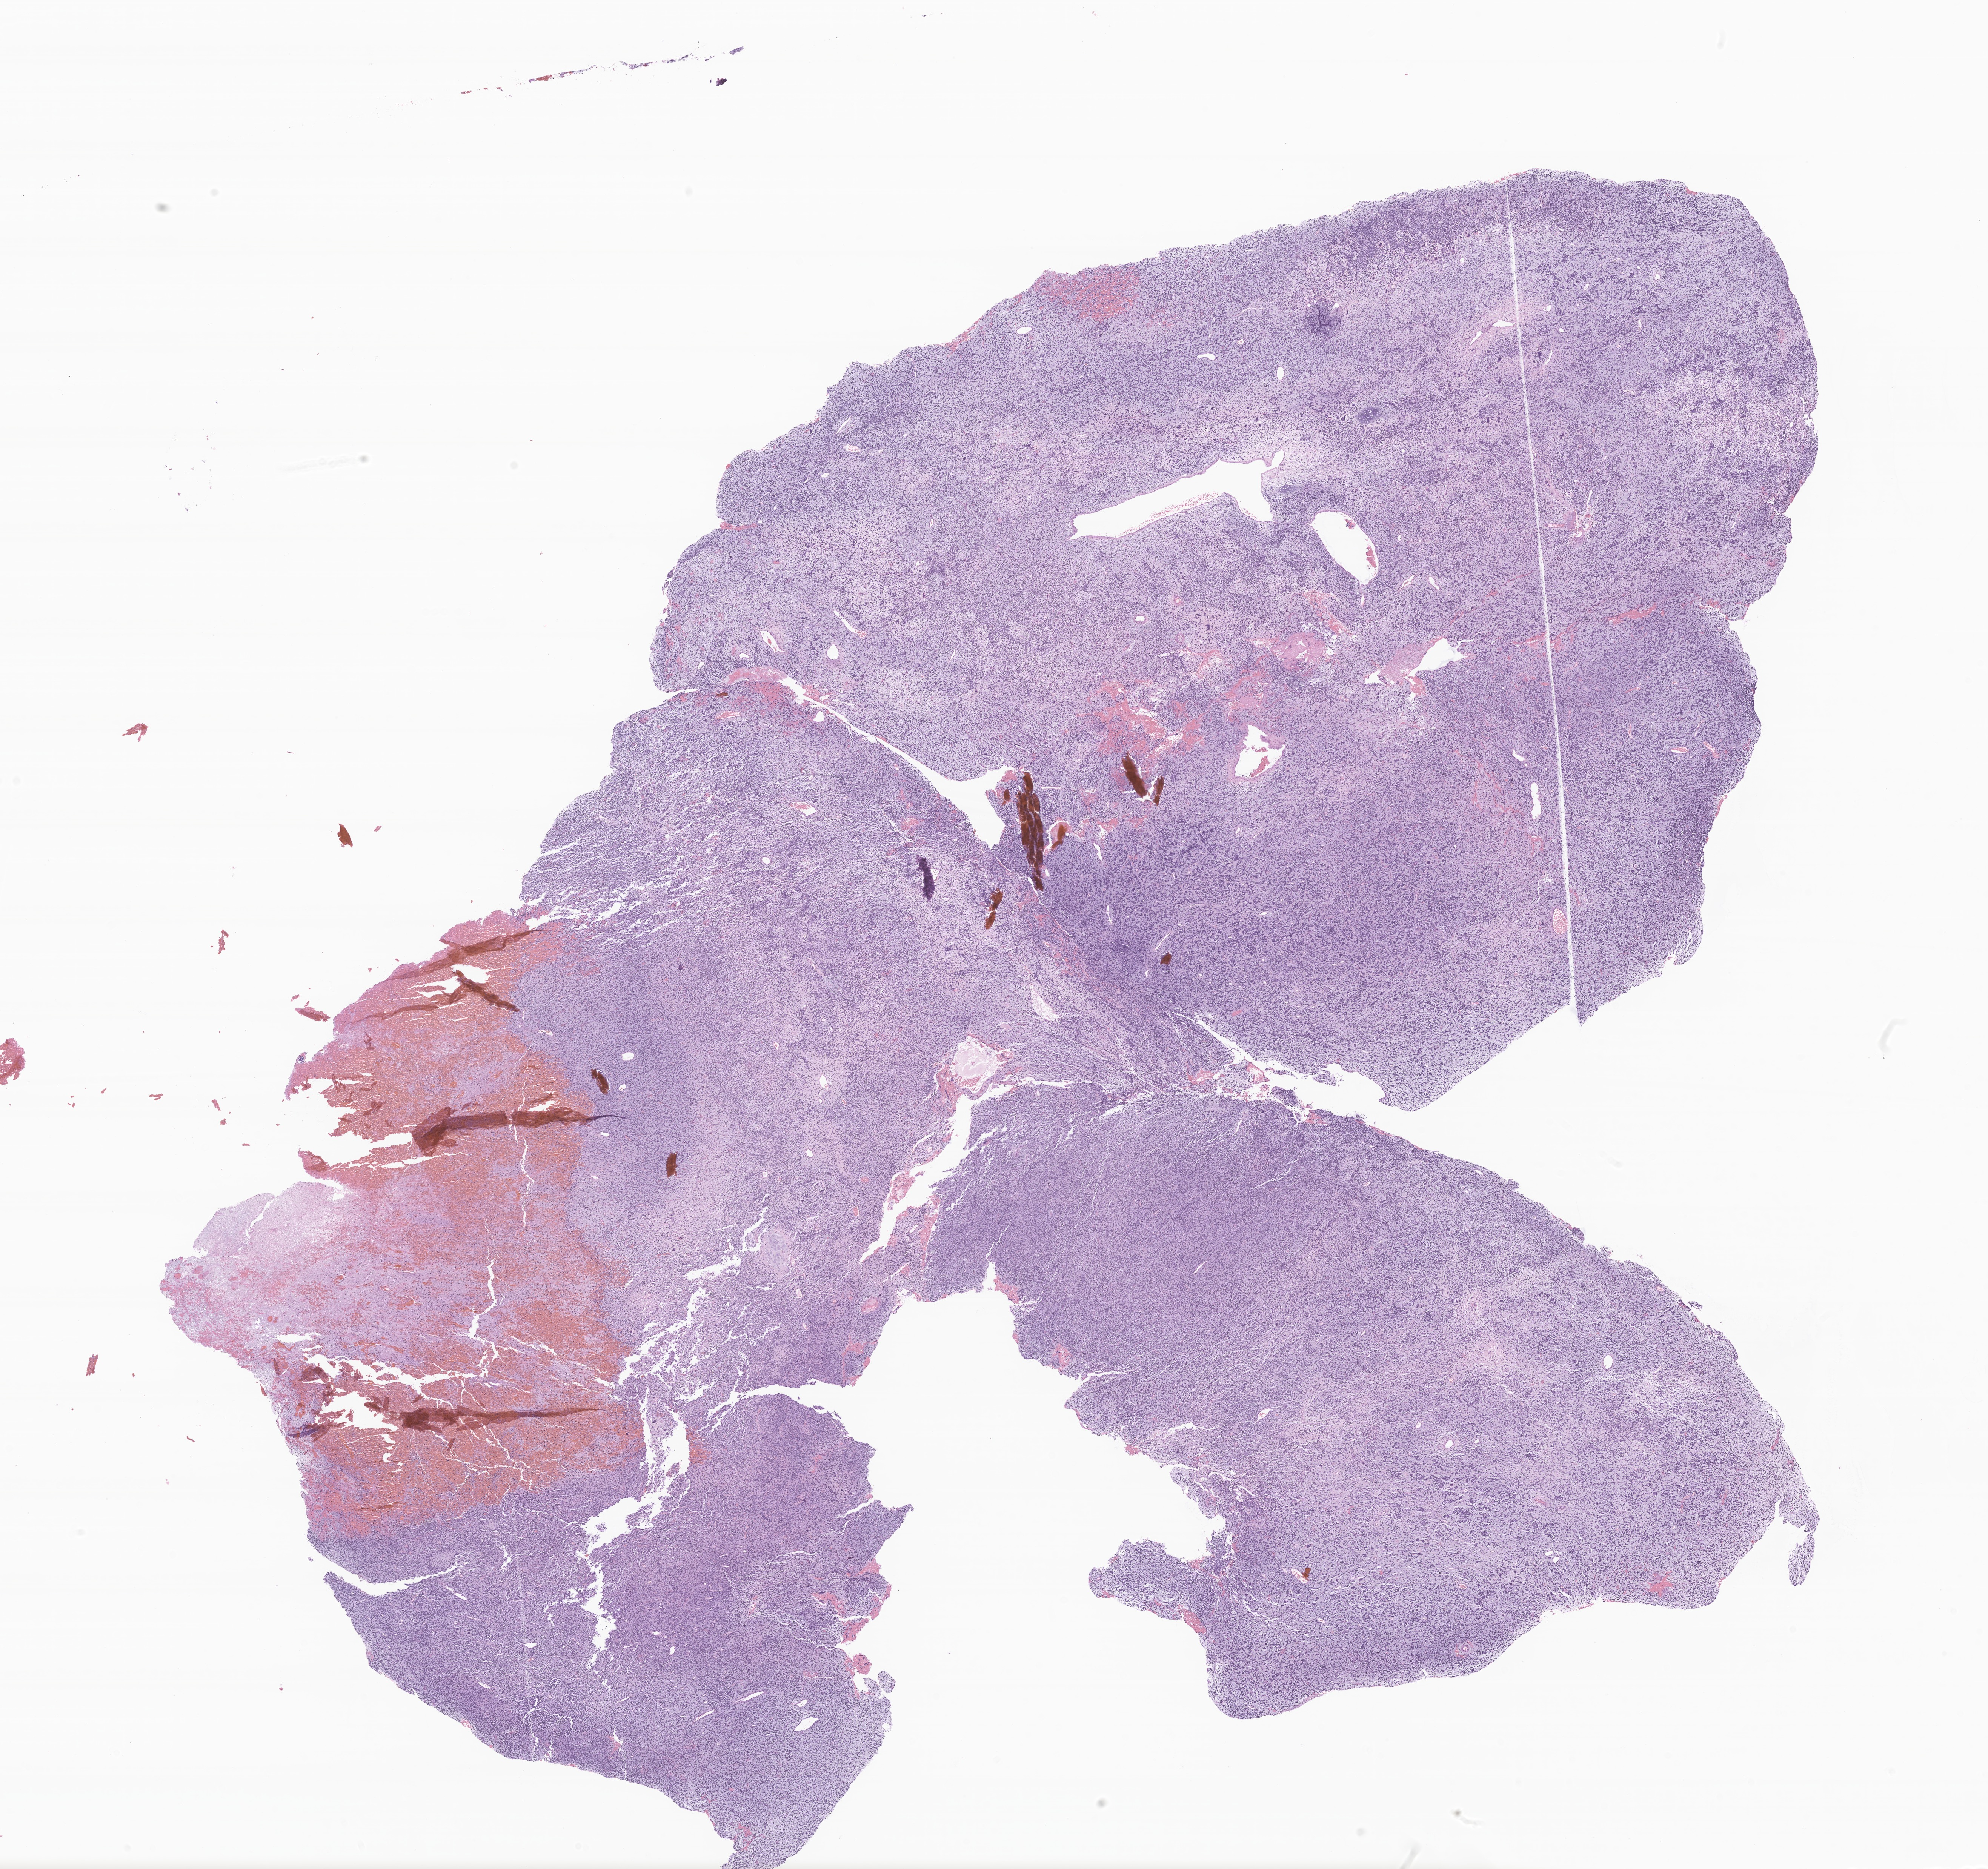
Digitized H&E-stained section of tumor tissue from the lower lobe of lung — low-resolution overview of the scanned area, about 22.2 x 20.9 mm; formalin-fixed, paraffin-embedded (FFPE) tissue. Patient: female, age 50 months (4 years 2 months).
Tissue or organ of origin (case record): lower lobe, lung. Diagnosis (ICD-O-3 morphology term): Pleuropulmonary blastoma.